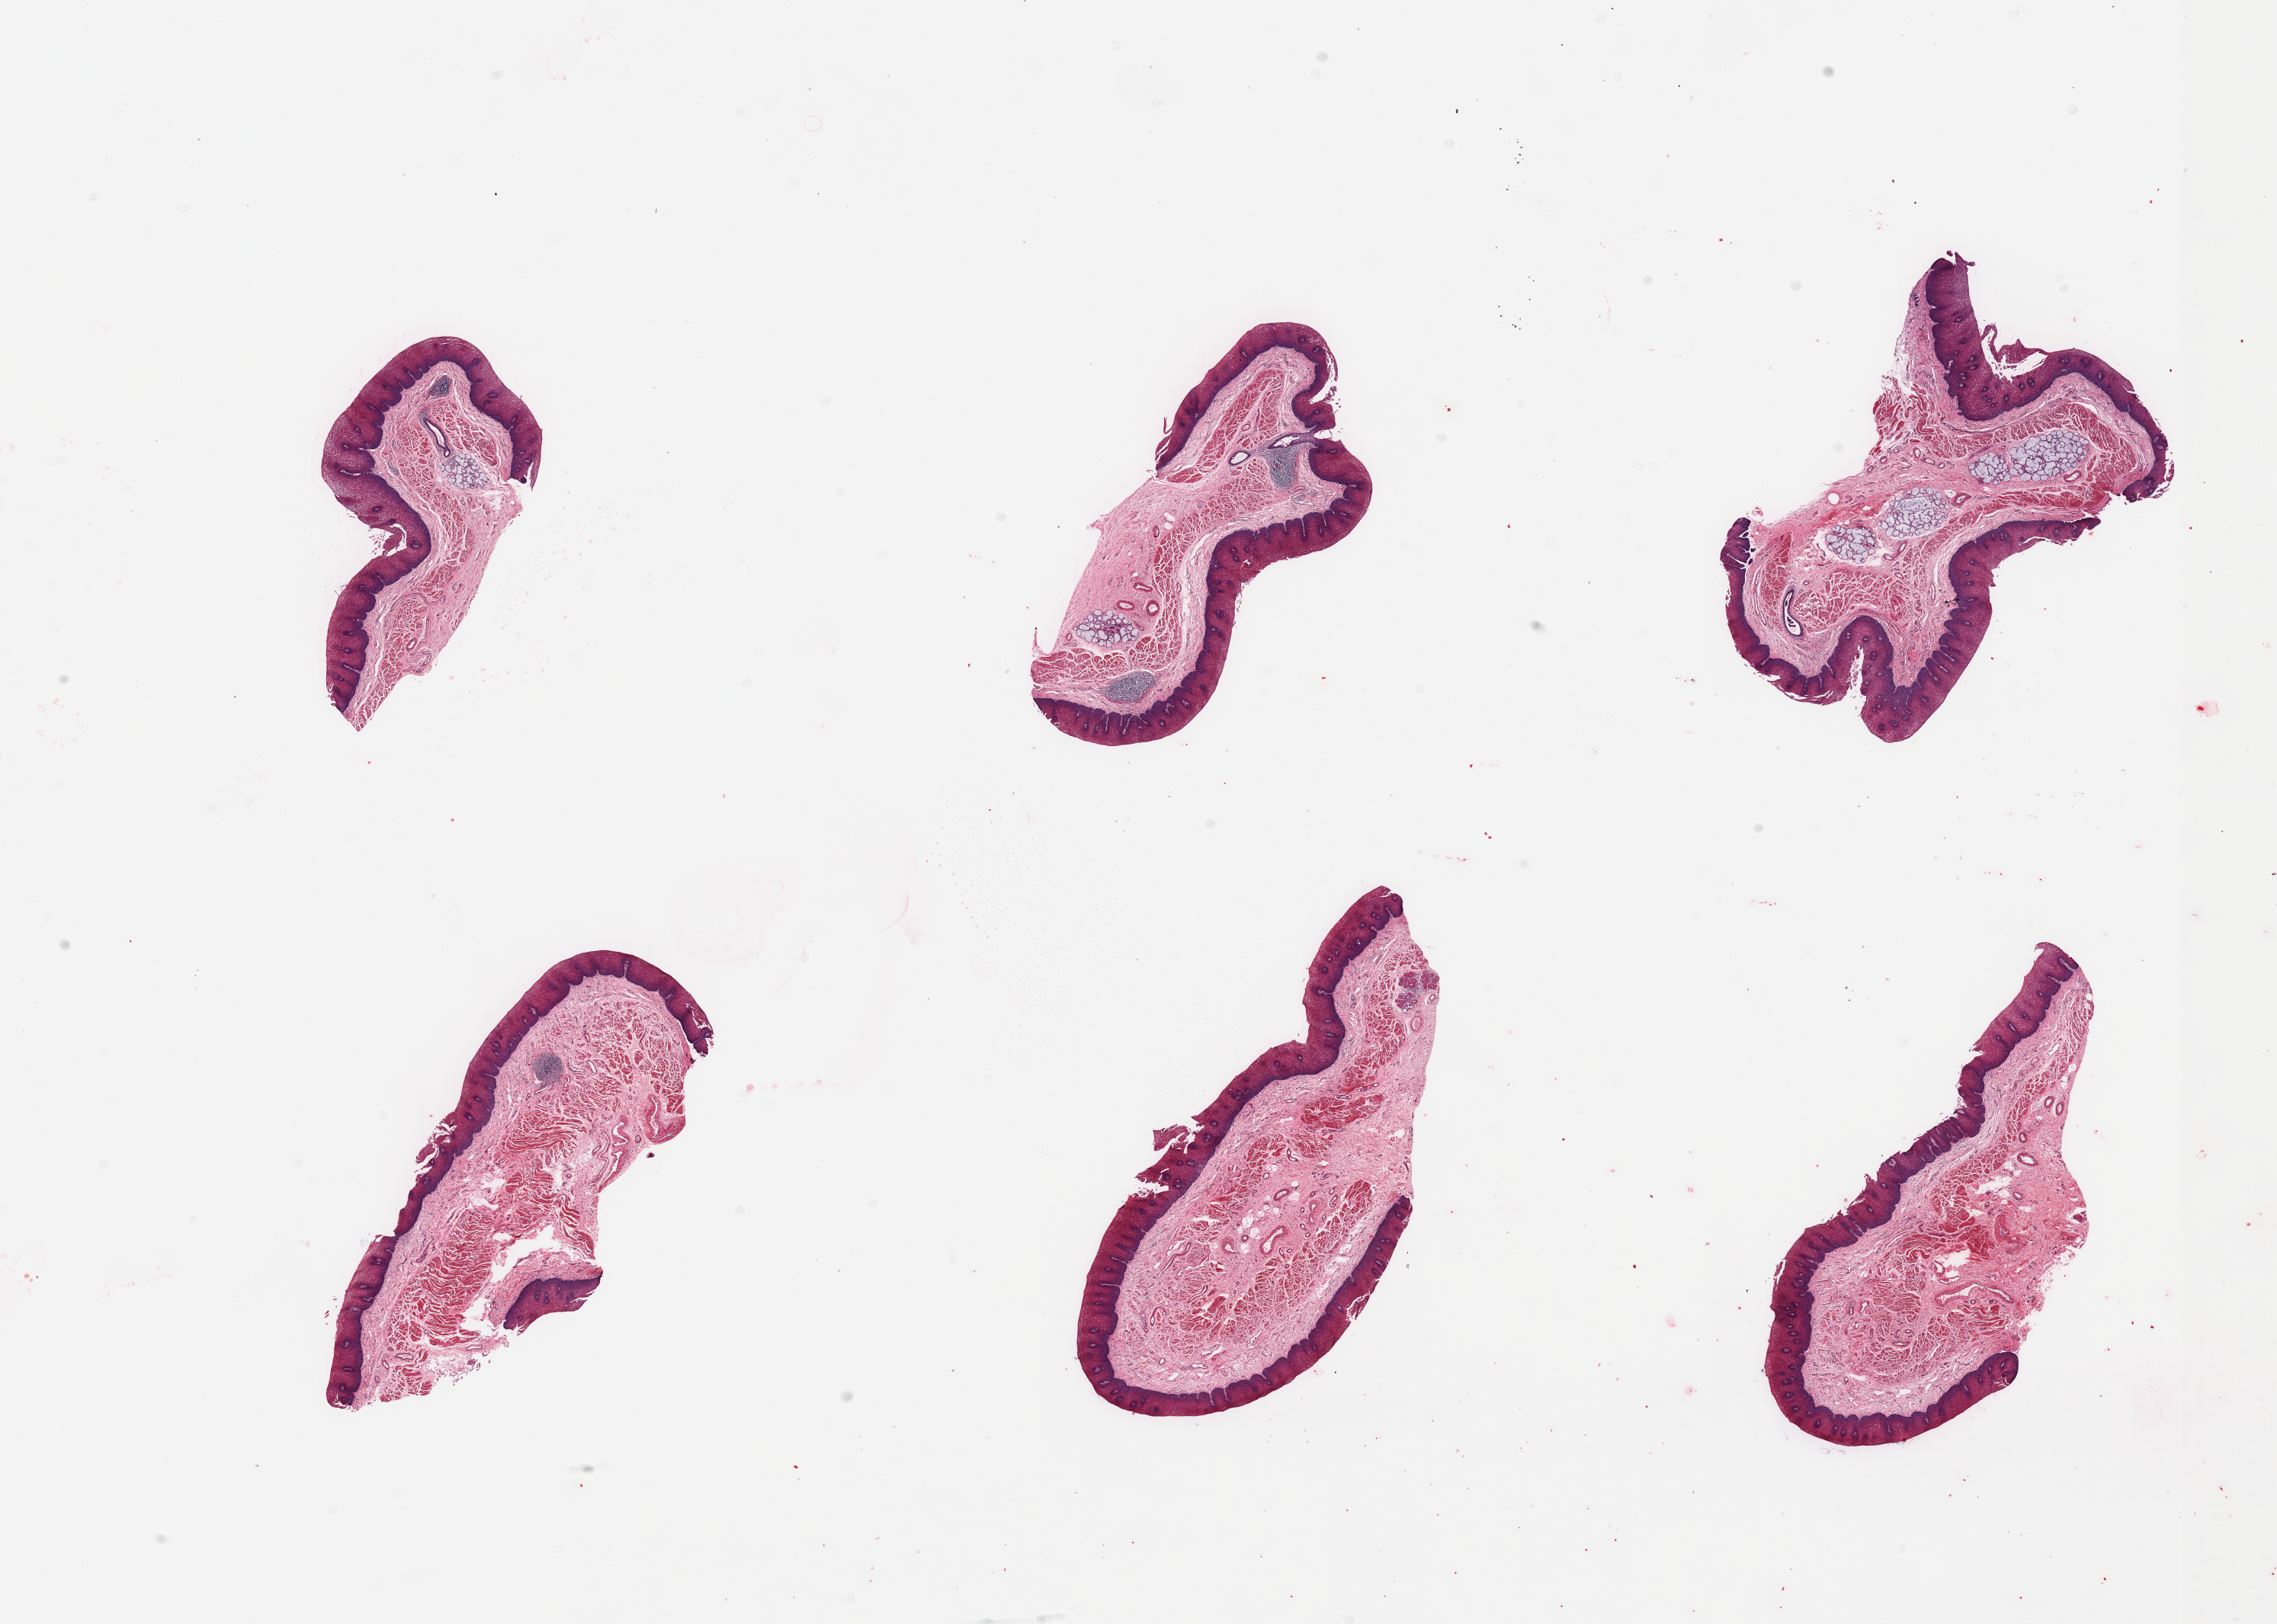
Whole-slide image, hematoxylin and eosin (H&E) stain — whole scanned area (about 23.6 x 16.9 mm, slide scanned at 20x) shown as a low-resolution overview. PAXgene-fixed, paraffin-embedded tissue. Target tissue: esophageal mucous membrane. Donor tissue sample. Male donor.
- reviewer comment on this tissue sample: 6 pieces, squamous mucosa up to ~0.5mm, well preserved; few submucosal mucus glands